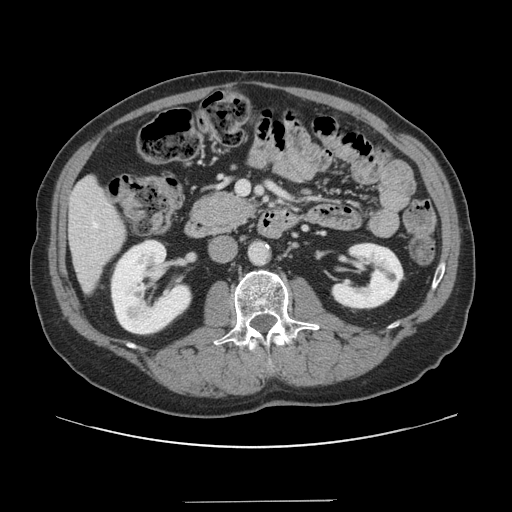
Contrast-enhanced abdominal CT, one axial slice; intravenous contrast given; soft-tissue window (W 400 / L 40 HU); 512 × 512 image matrix, field of view 399 × 399 mm. Male patient, age 63 years. From the clinical record (not read from this slice): diagnosis: colorectal cancer liver metastases, imaged before liver resection; multiple liver metastases: no; largest metastasis: 2.1 cm; disease in both lobes: no.
Outlined on this slice (manually delineated by an expert):
- hepatic veins: box from (x=94, y=223) to (x=98, y=228) px
- liver: (x=70, y=178)–(x=125, y=290)
- planned liver remnant (the part of the liver to remain after resection): (x=70, y=178)–(x=125, y=290)
- portal vein (with intrahepatic branches): (x=237, y=182)–(x=249, y=194)